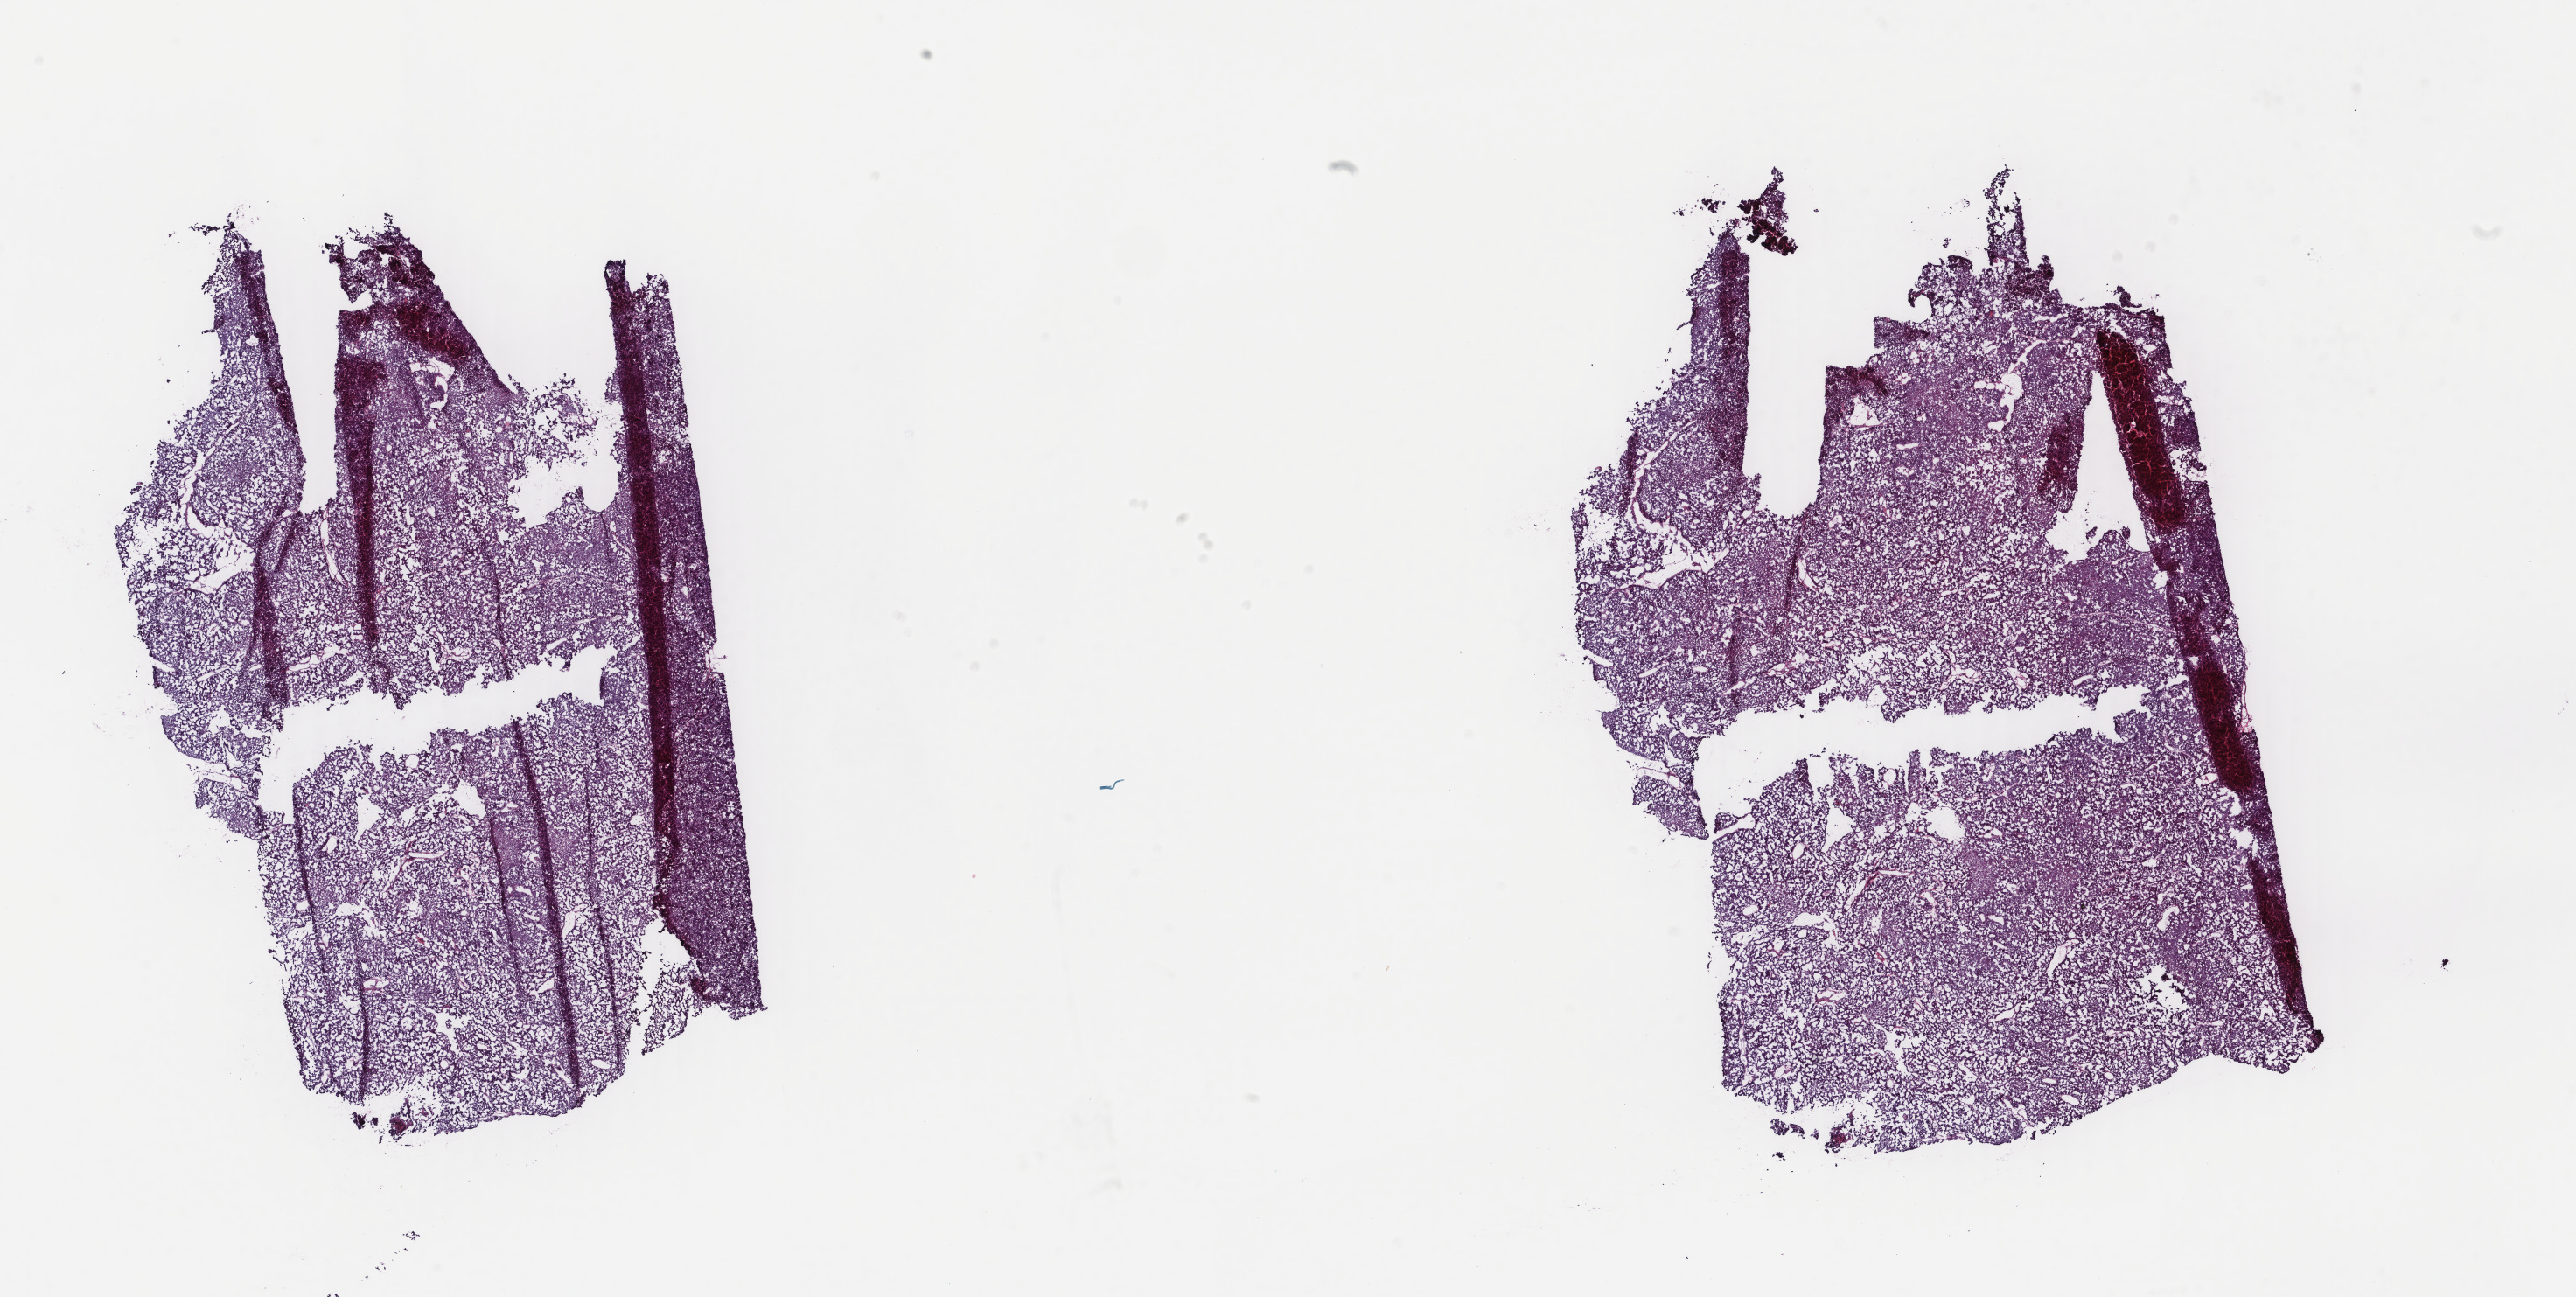
H&E-stained whole-slide image — shown as a low-resolution overview of the whole scanned area (about 23.4 x 11.8 mm), frozen section, breast, primary tumour sample. Female, age 72 years at initial diagnosis. Pathologist review of this section (percent, as recorded): tumour cells 96%, tumour nuclei 96%, normal cells 0%, stromal cells 4%, necrosis 0%. Inflammatory infiltration, as recorded: lymphocyte infiltration 1%, monocyte infiltration 0%, neutrophil infiltration 0%.
AJCC pathologic stage: IIA. Lymph nodes positive (case pathology): 0 of 5 examined. Histologic diagnosis: Papillary carcinoma, NOS. TNM: T2 N0 (i-) M0.